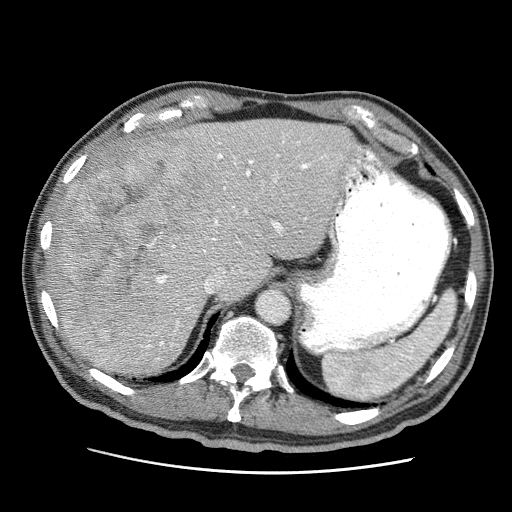
Contrast-enhanced abdominal CT (liver protocol), one axial slice; slice 44 of 75 in the series (ordered by position); reconstruction kernel STANDARD; soft-tissue window (W 400 / L 40 HU); 2.5 mm slice thickness; 512 × 512 image matrix, field of view 360 × 360 mm. From the clinical record (not read from this slice): diagnosis: hepatocellular carcinoma (patient treated with transarterial chemoembolisation; whether this scan precedes or follows treatment is not stated here); TNM stage (as recorded): Stage-IIIA; Child-Pugh class: A; tumour differentiation: well differentiated.
Outlined on this slice (semi-automatic segmentation, software-assisted and operator-edited):
- abdominal aorta: bounding box [x1, y1, x2, y2] px = [256, 289, 290, 323]
- liver parenchyma outside the tumour (the mass and vessels are separate outlines, so this box may not span the whole liver): [47, 118, 364, 374]
- mass: [50, 137, 217, 358]
- liver vessels: [65, 133, 361, 361]